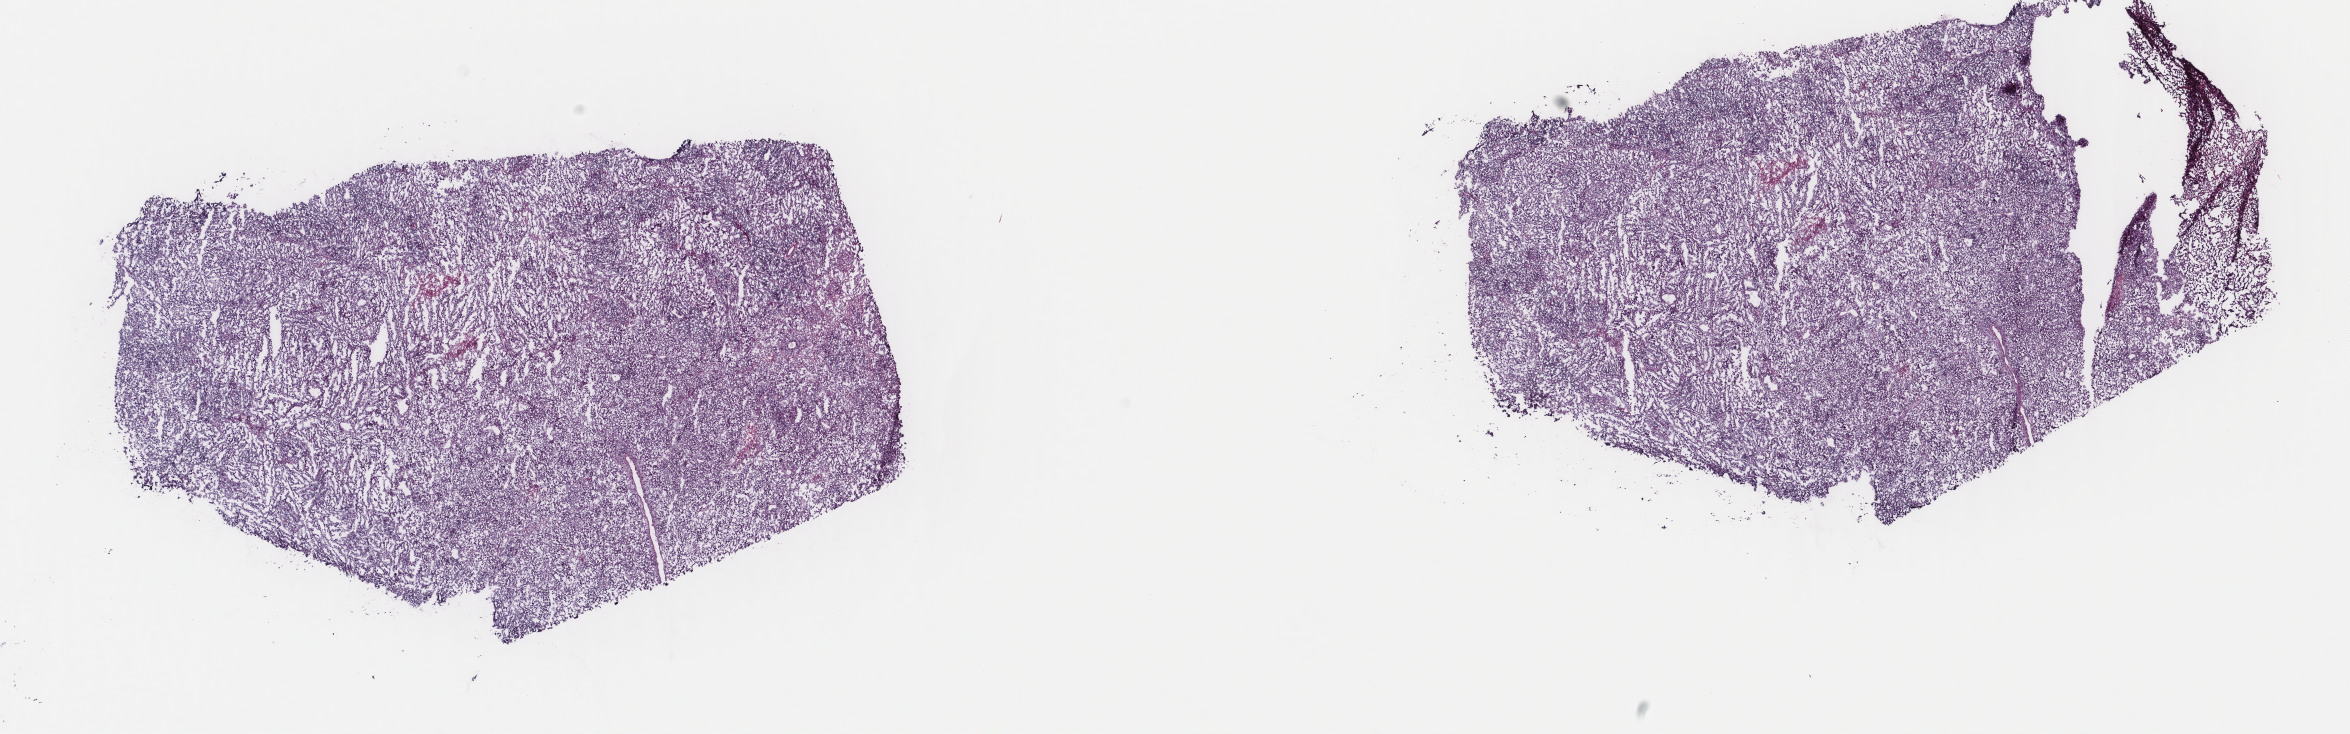
Whole-slide histology image, Hematoxylin and eosin (H&E) stained, shown as a low-resolution overview of the whole scanned area (about 18.7 x 5.8 mm, slide scanned at 40x); frozen section from the top of the tissue portion; metastatic tumour sample, sampled site: lymph nodes of inguinal region or leg. Patient: male, age at initial diagnosis 43 years. Composition of this section per pathologist review: tumour cells 88%, tumour nuclei 60%, normal cells 0%, stromal cells 2%, necrosis 10%. Inflammatory infiltration, as recorded: lymphocyte infiltration 35%, monocyte infiltration 1%, neutrophil infiltration 0%.
This section: metastatic tumour tissue. Patient diagnosis: Malignant melanoma, NOS.